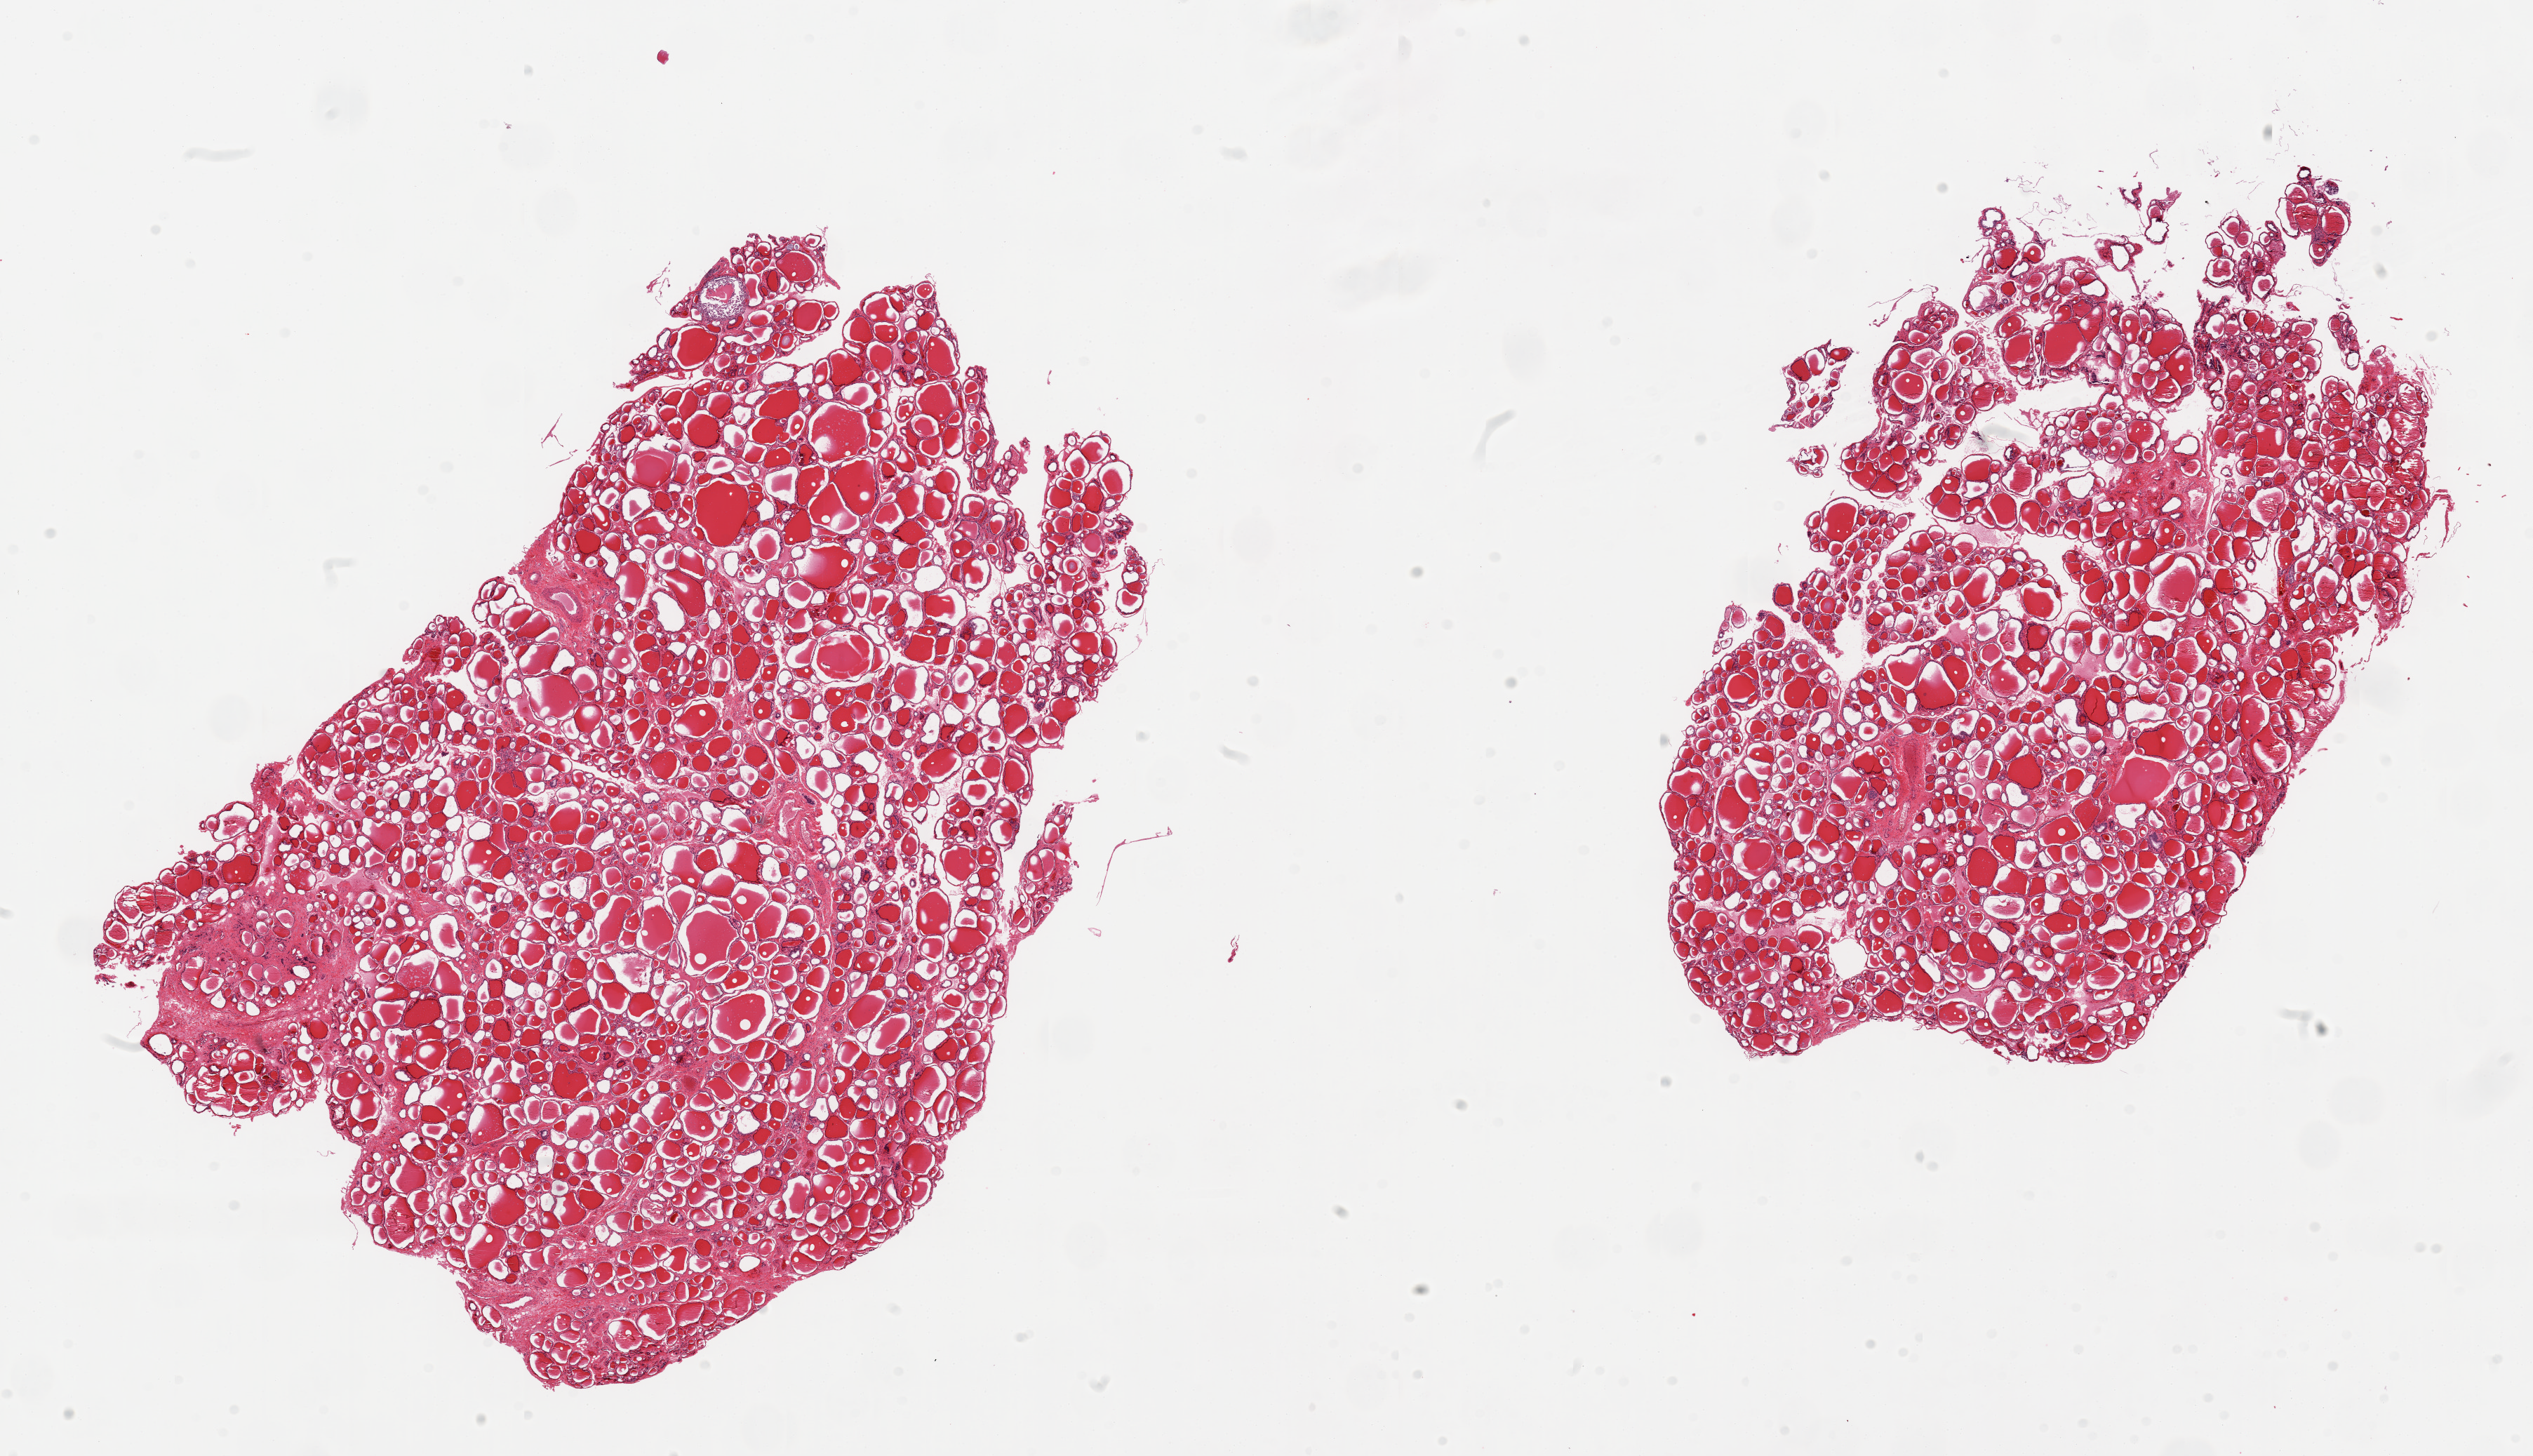
Haematoxylin and eosin whole-slide image, low-resolution overview of the scanned area, about 28.5 x 16.4 mm. PAXgene-fixed, paraffin-embedded tissue. Section of thyroid (target tissue). Tissue donor sample. Donor: female.
Reviewer comment on this tissue sample: 2 pieces.